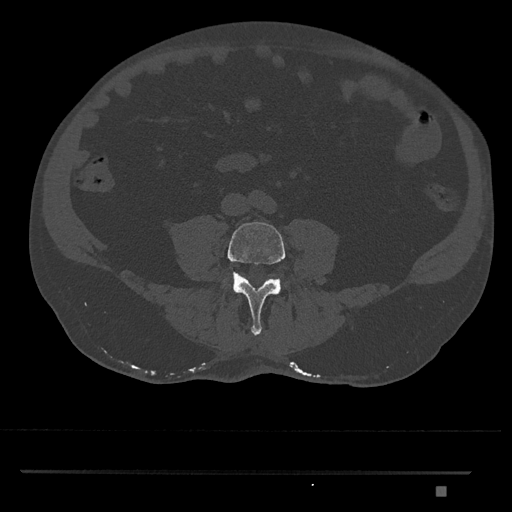
CT including the spine, one axial slice. Position 609 of 1134 along the scan axis. 120 kVp. Bone window (W 1800 / L 400 HU). 0.5 mm slice thickness. 512 × 512 image matrix, field of view 429 × 429 mm. Patient: male, 65 years. From the clinical record (not read from this slice): primary cancer: prostate.
Annotated regions visible in this slice (semi-automatically segmented with operator editing):
- L4 vertebra: box from (x=220, y=221) to (x=286, y=335) px